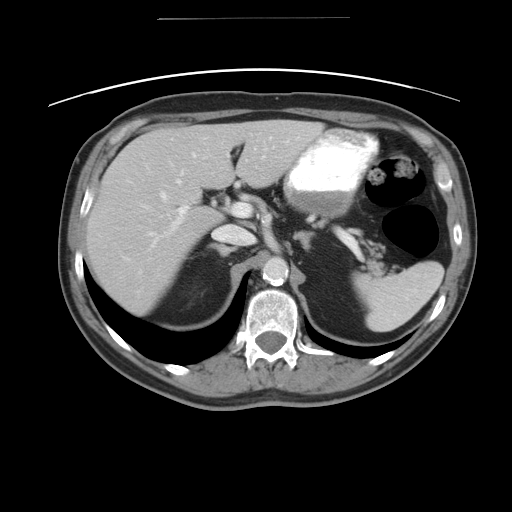
Contrast-enhanced abdominal CT, one axial slice; slice 29 of 49 in the series (ordered by position); 120 kVp; intravenous contrast given; soft-tissue window (W 400 / L 40 HU); 512 × 512 image matrix, field of view 413 × 413 mm. Male patient, age 57 years. From the clinical record (not read from this slice): diagnosis: colorectal cancer liver metastases, imaged before liver resection; multiple liver metastases: yes; largest metastasis: 4 cm; disease in both lobes: no.
Structures marked on this image (outlined manually by an expert reader):
- hepatic veins: bounding box [x1, y1, x2, y2] px = [124, 152, 194, 271]
- liver: [86, 119, 323, 314]
- planned liver remnant (the part of the liver to remain after resection): [210, 119, 323, 189]
- portal vein (with intrahepatic branches): [147, 178, 249, 246]